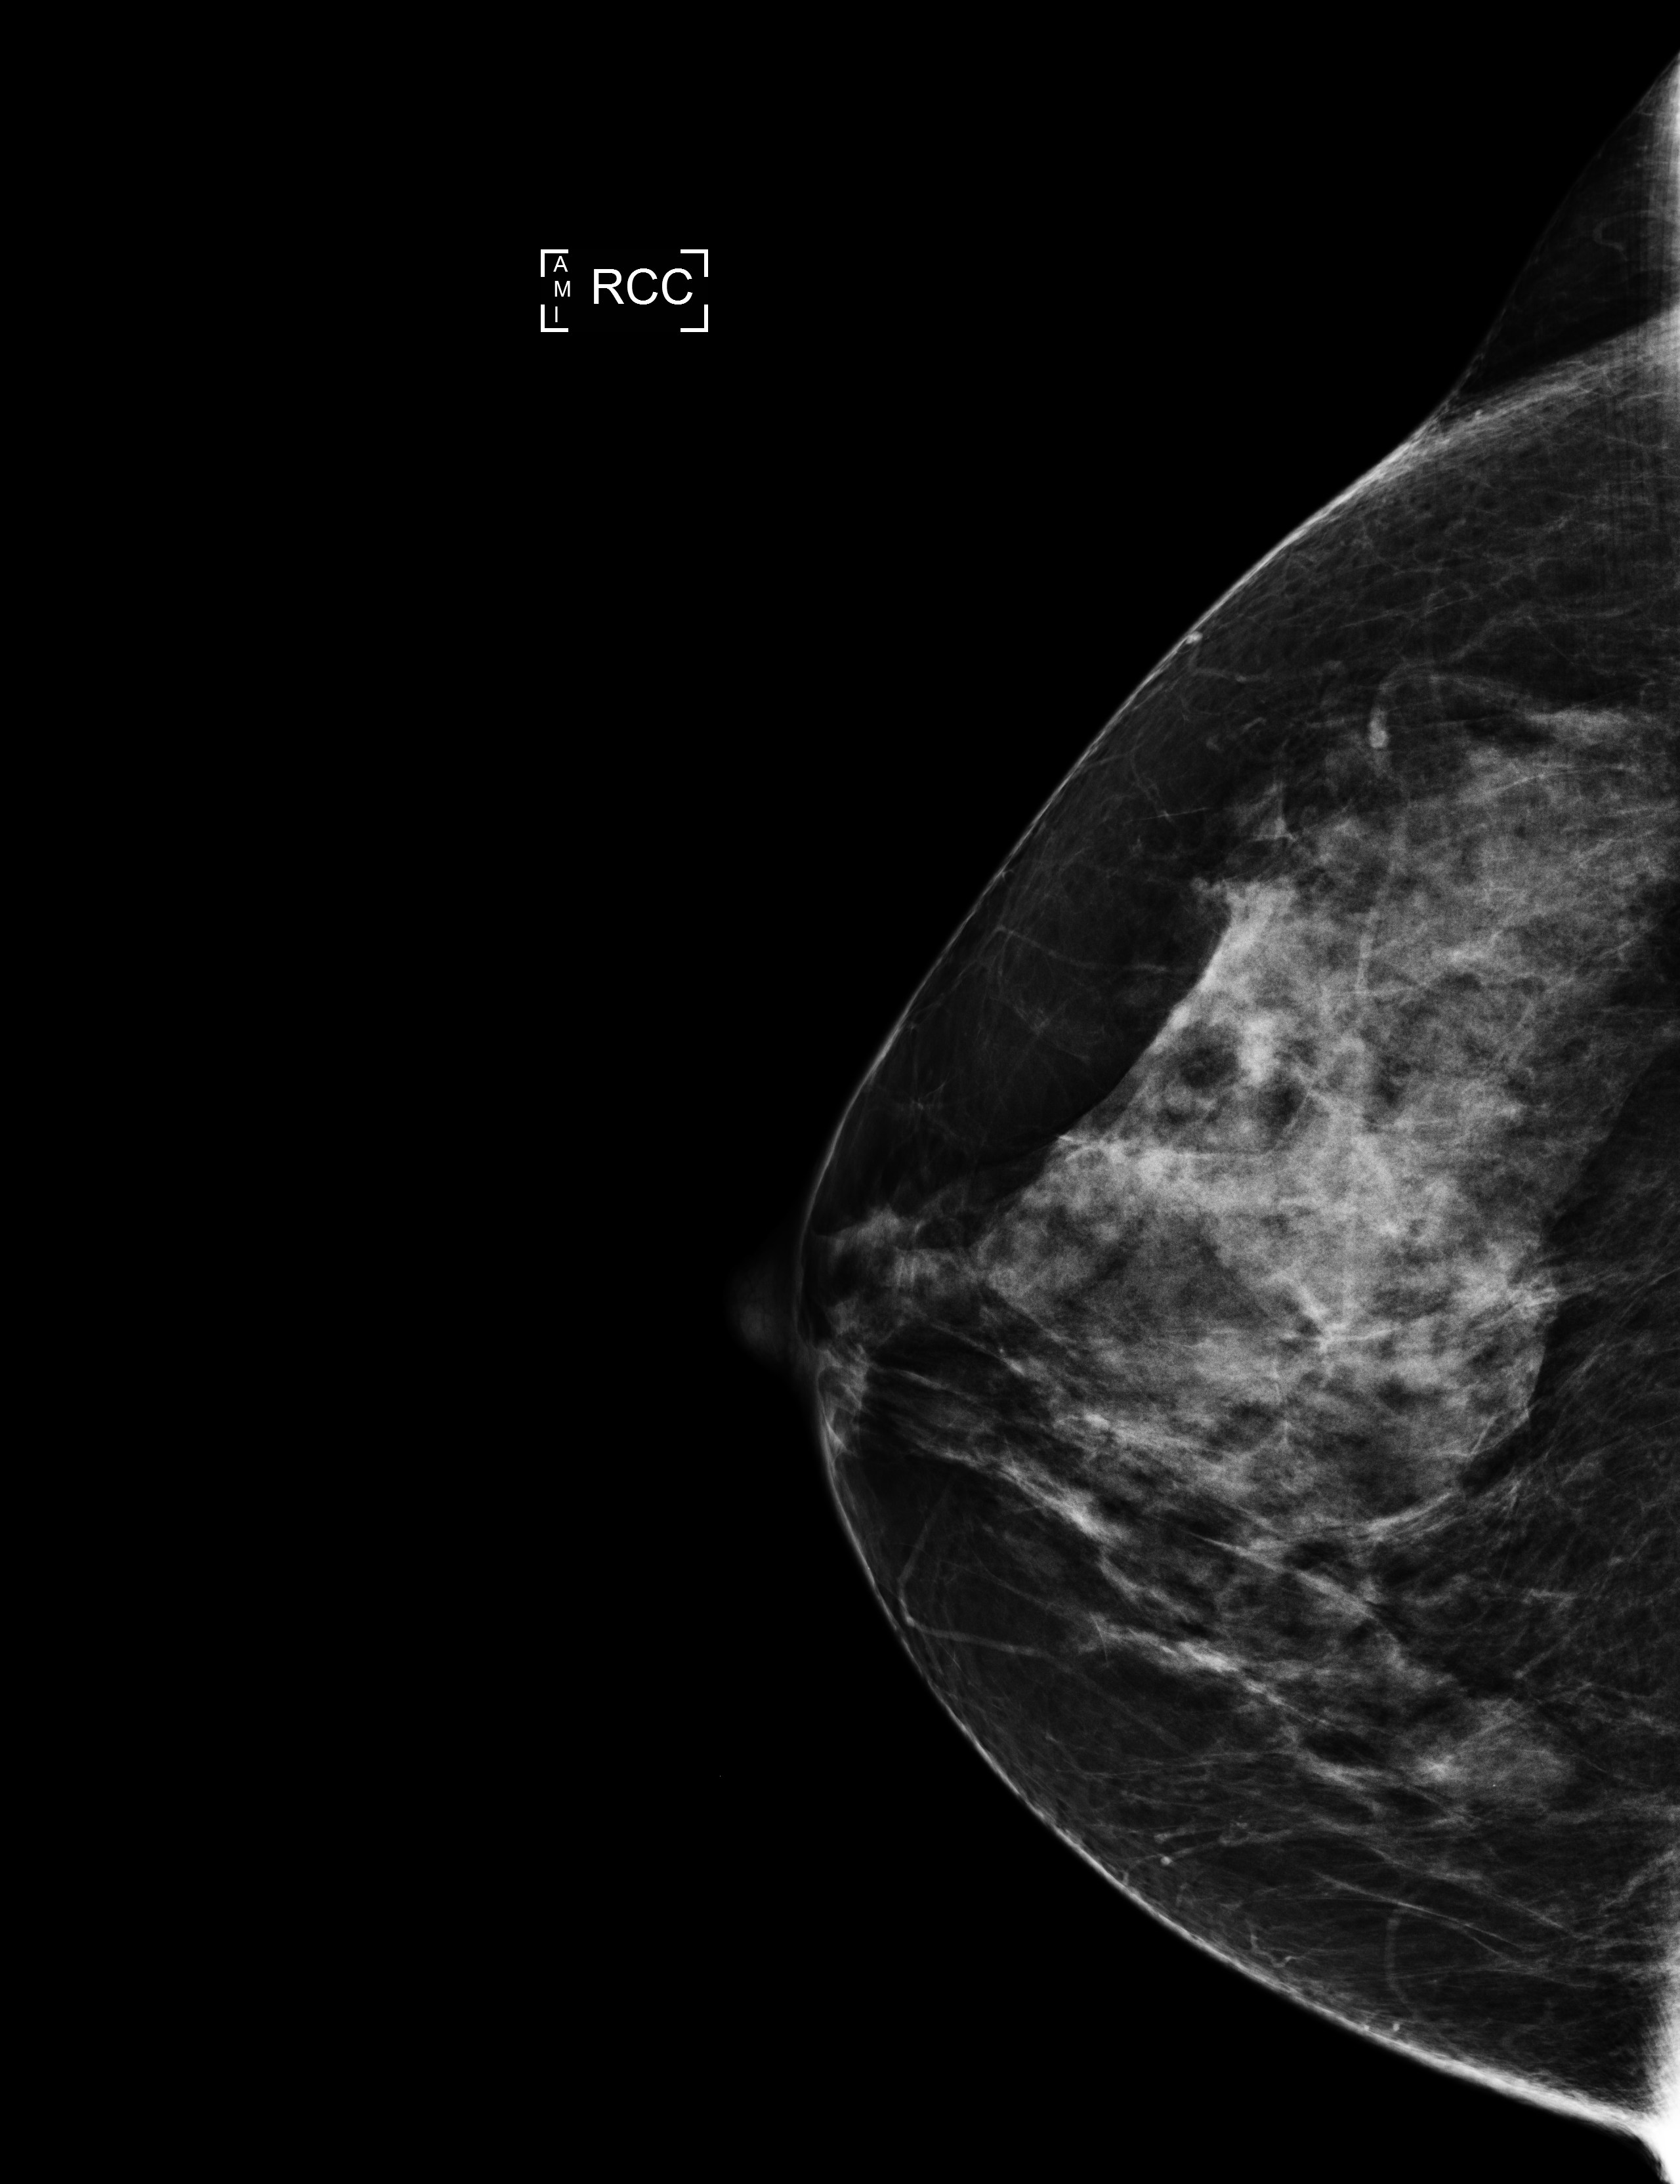
Screening examination.
Image type: full-field digital mammogram. Breast: right. Projection: CC view.